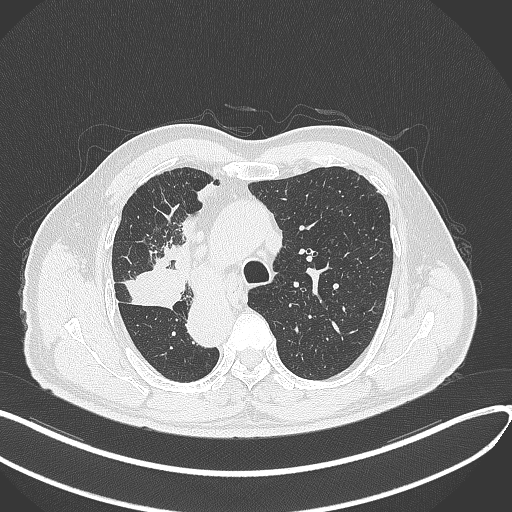
Chest CT, one axial slice; position 220 of 300 along the scan axis; lung window (W 1500 / L -600 HU); 1 mm slice thickness; 512 × 512 image matrix, field of view 400 × 400 mm. Male patient, age 67 years. From the clinical record (not read from this slice): clinical TNM (as recorded): T2a N0 M0.
Annotated regions visible in this slice (rectangle marked by the reading radiologist):
- lung tumour (recorded histology: squamous cell carcinoma): bounding box (x1, y1, x2, y2) in pixels: (123, 259, 189, 312)